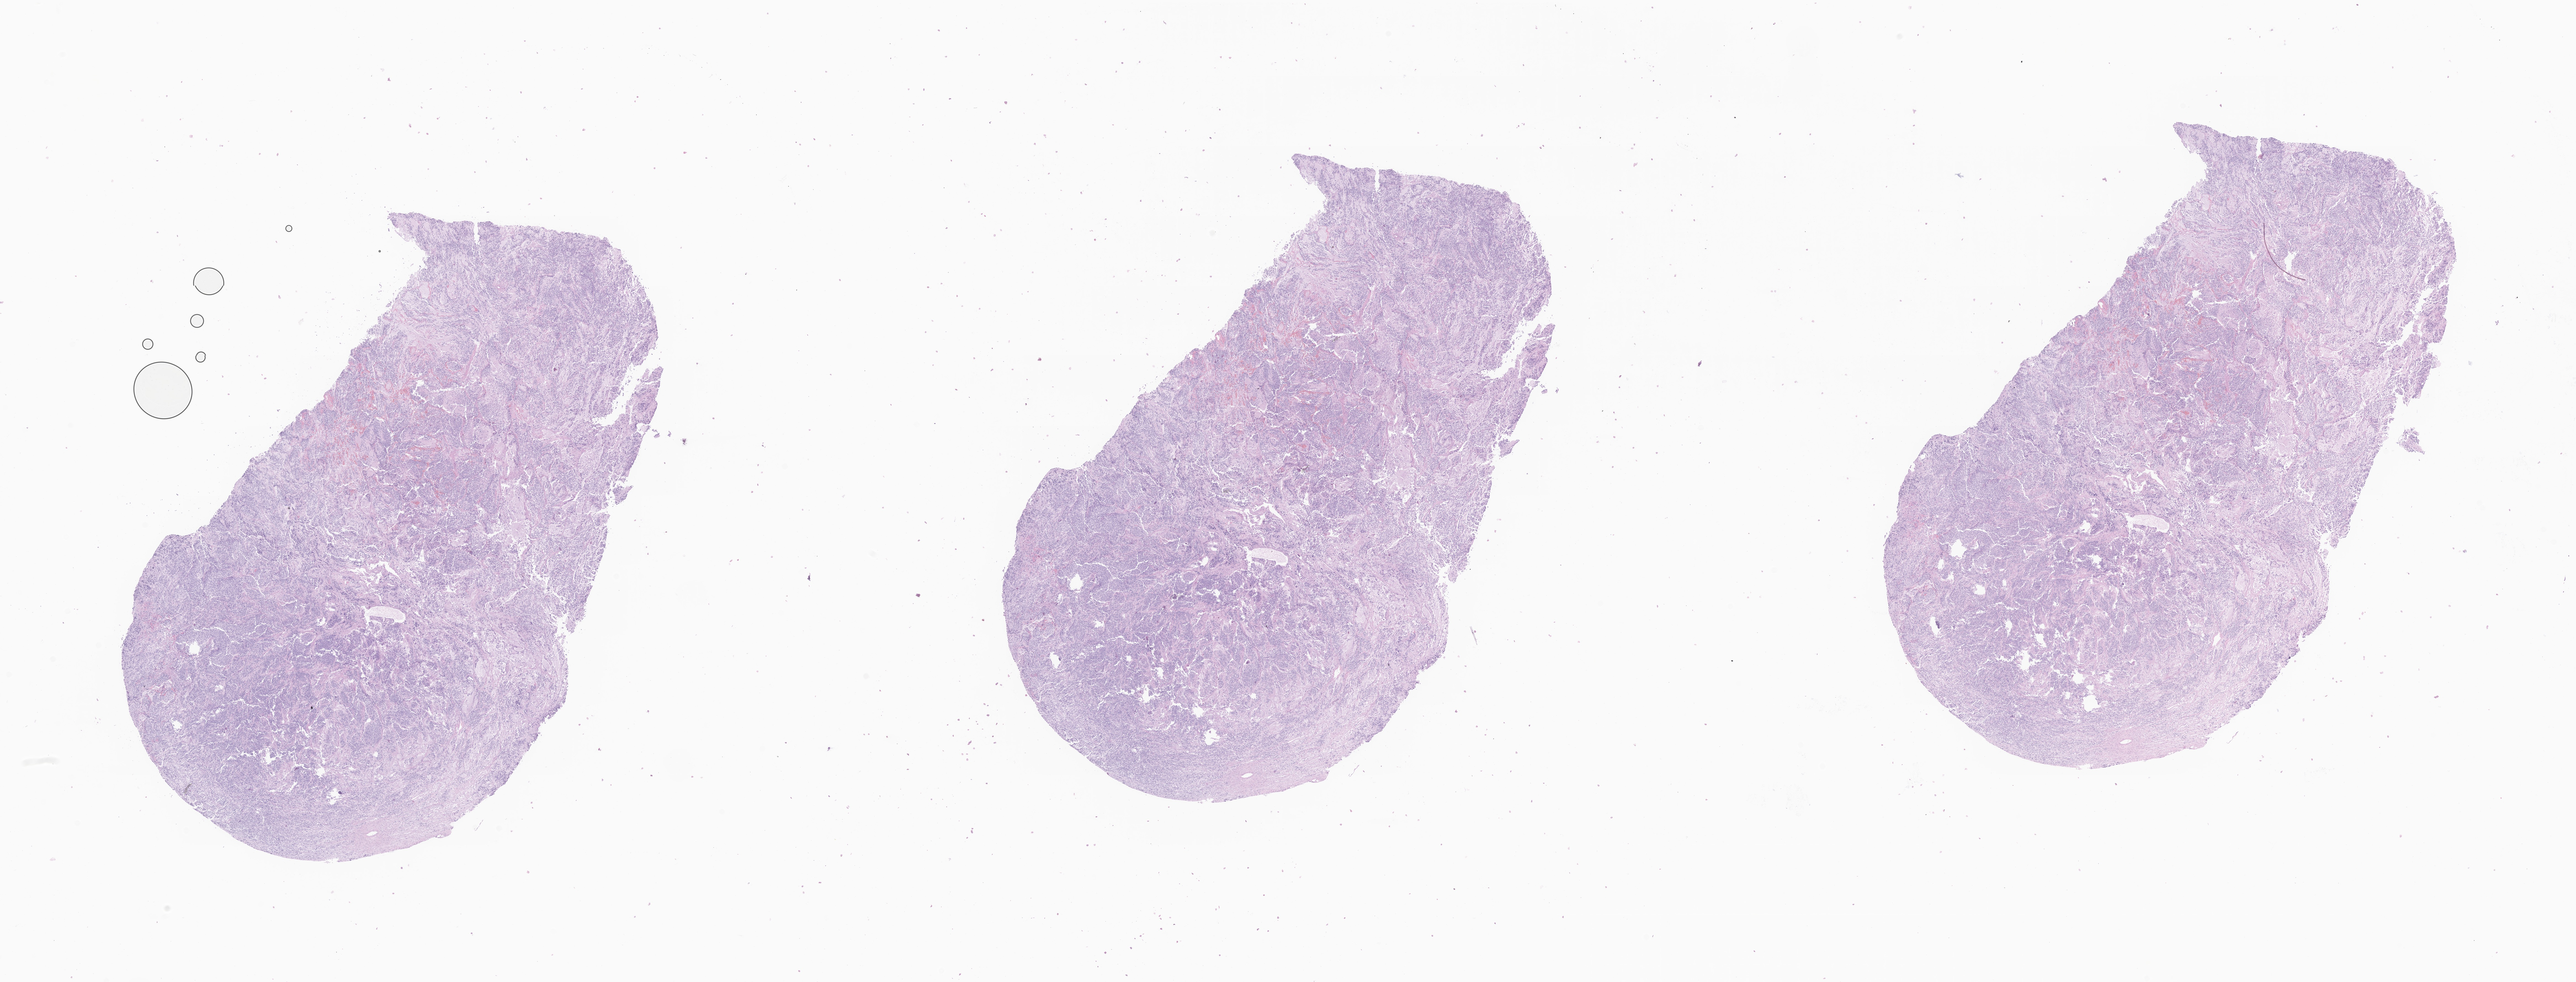
H&E whole-slide image of tumor tissue from the adrenal gland, low-resolution overview of the scanned area, about 39.3 x 15.0 mm. Formalin-fixed, paraffin-embedded (FFPE) tissue. Patient: female, age 108 months (9 years).
- diagnosis: Neuroblastoma, NOS